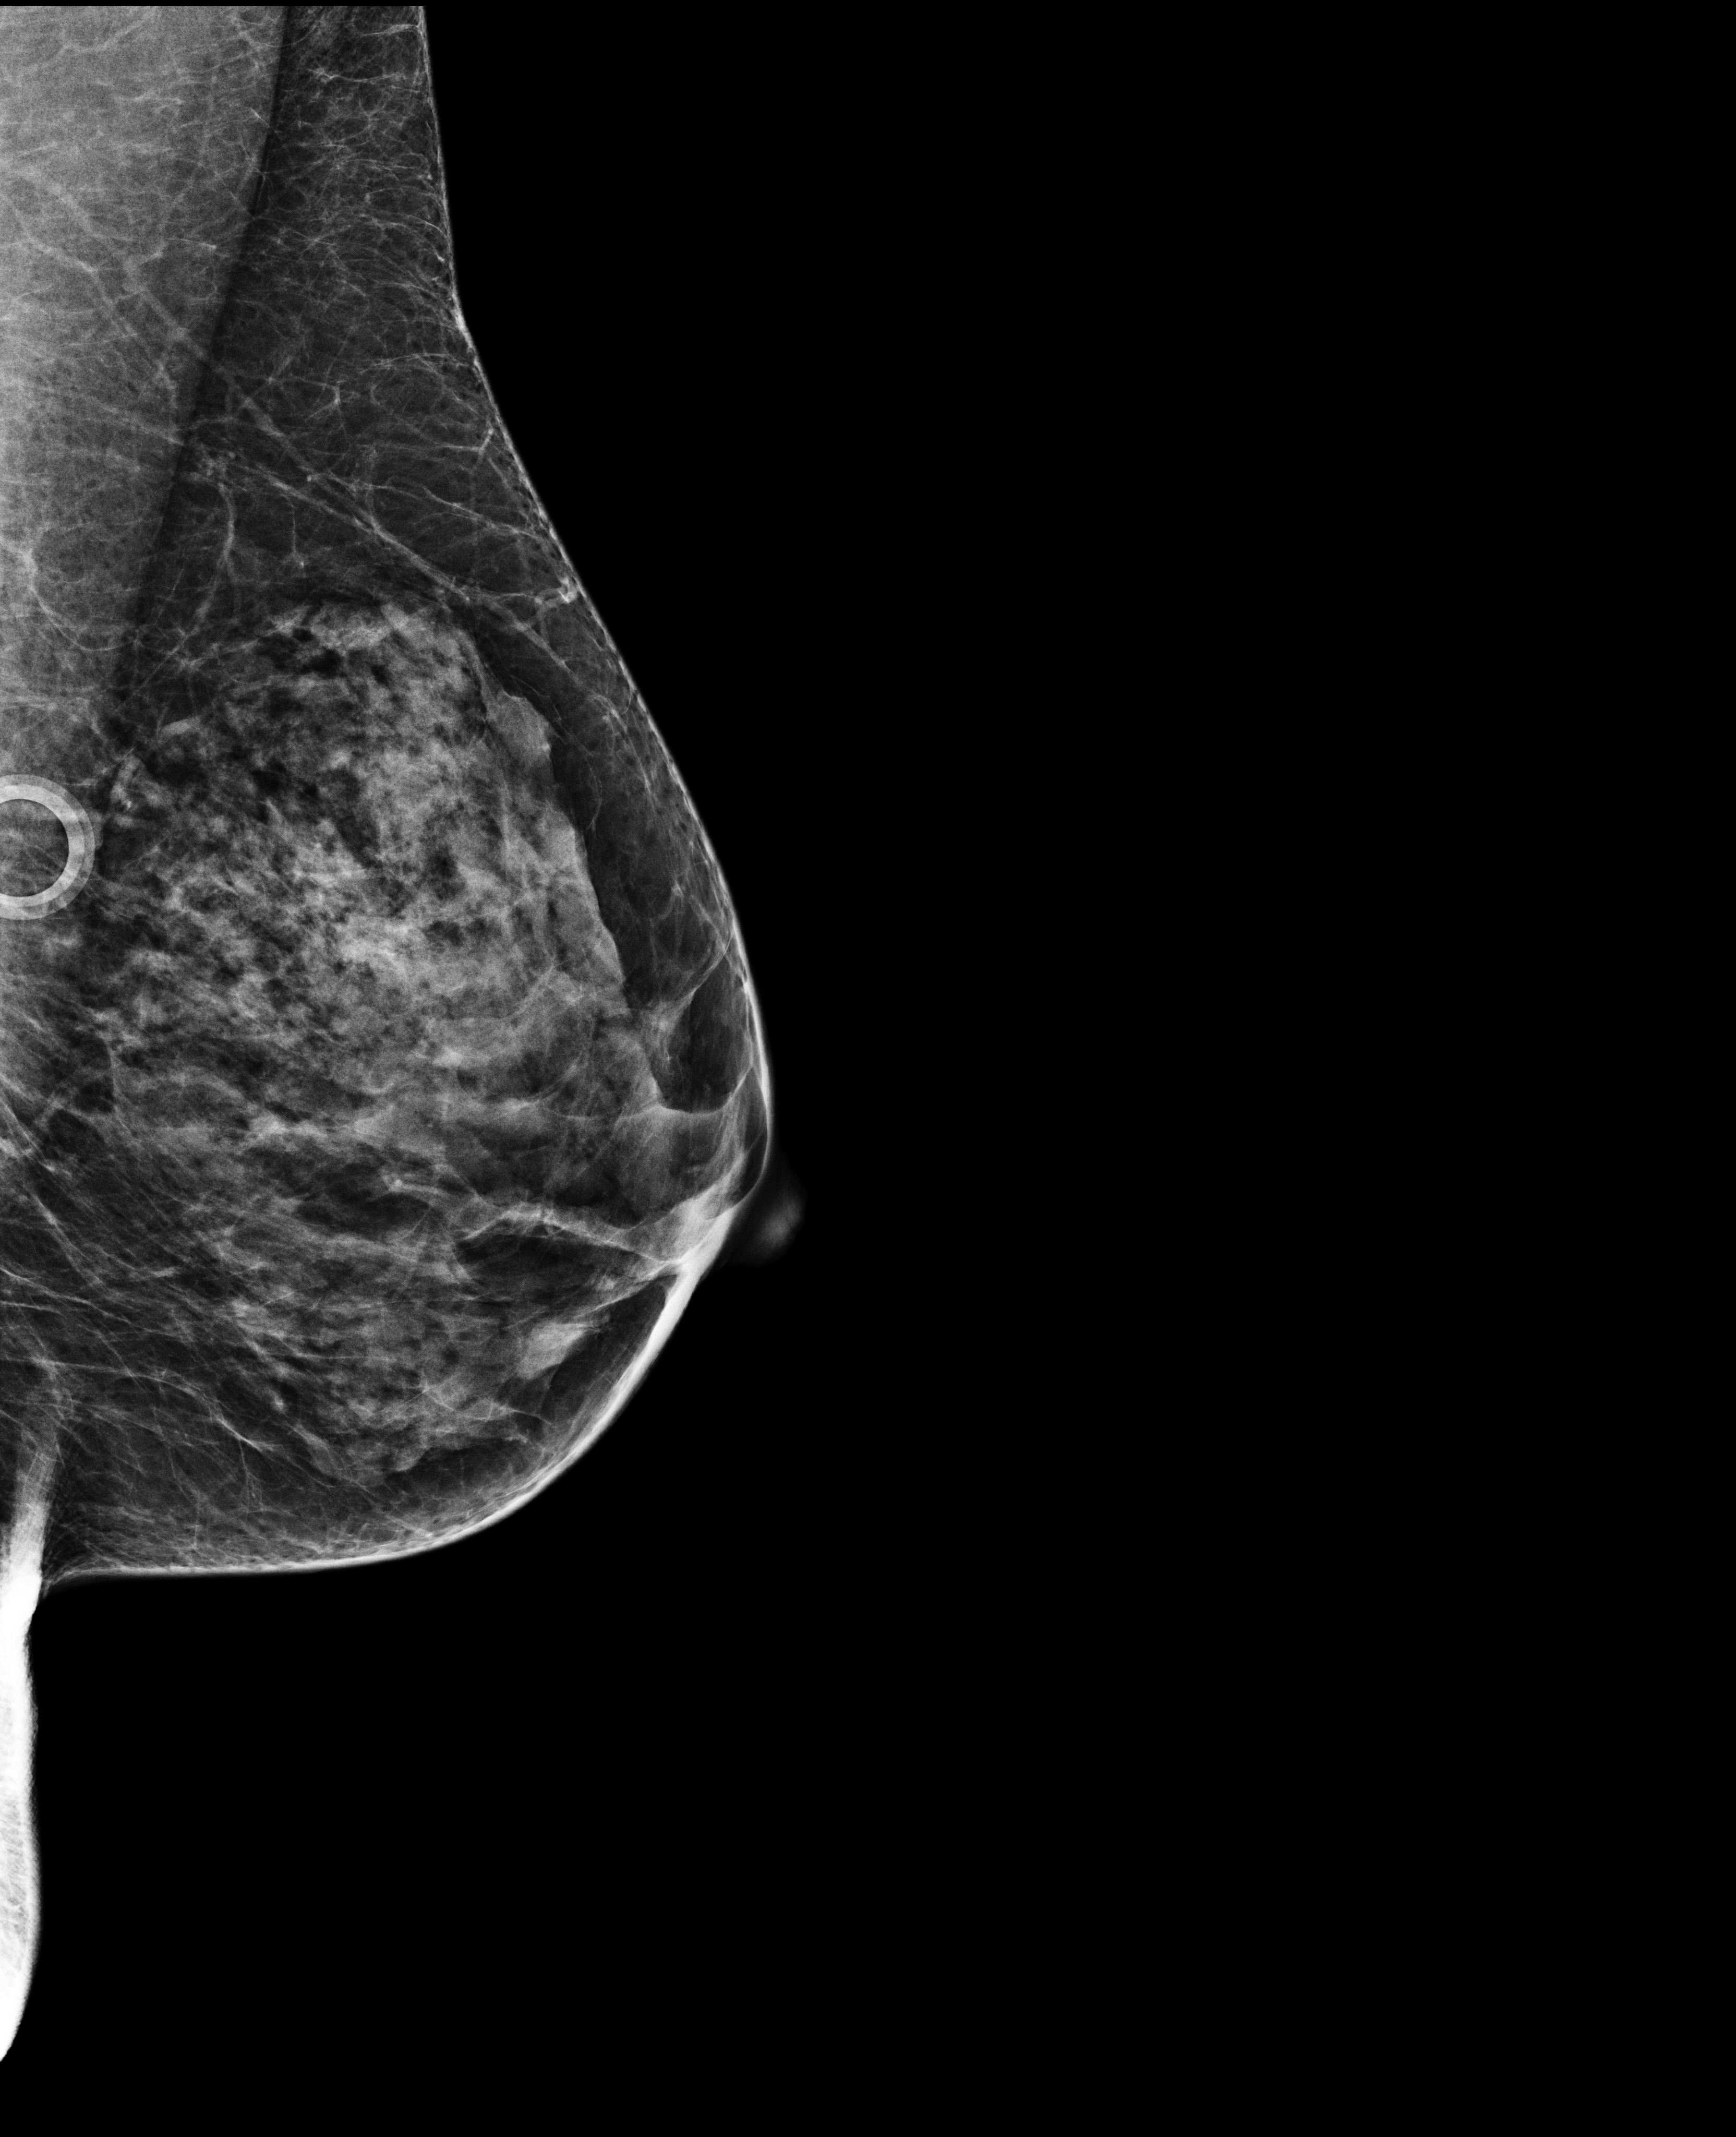
Digital mammogram (FFDM); left breast; MLO view; screening examination; compressed breast thickness 39 mm. Patient: female, 66 years.
BI-RADS breast density category at the screening exam (both breasts, scale 1–4): 3. Final BI-RADS category for the screening round (tomosynthesis exam, both breasts): category 1. Recall: no recall after this screen.